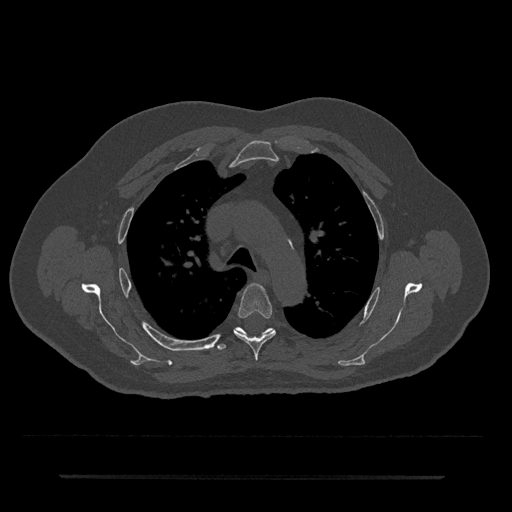
CT including the spine, one axial slice. Slice 518 of 797 in the series (ordered by position). Reconstruction kernel Br40s/3. 120 kVp. Bone window (W 1800 / L 400 HU). 0.5 mm slice thickness. 512 × 512 image matrix, field of view 437 × 437 mm. Male patient, age 69 years. Case-level facts recorded for this patient, not image findings: primary cancer: prostate.
Structures marked on this image (semi-automatic segmentation, software-assisted and operator-edited):
- T4 vertebra: box from (x=234, y=284) to (x=276, y=361) px
- T5 vertebra: (x=217, y=327)–(x=274, y=350)